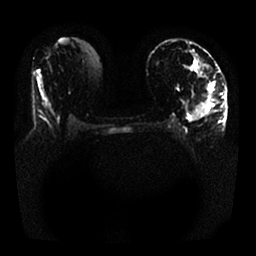
Breast MRI, one axial slice. Position 12 of 25 along the scan axis. Diffusion-weighted series; image 2 of 4 stored at this slice position (different b-values; order by instance number). 1.5 T. 4 mm slice thickness. 256 × 256 image matrix, field of view 340 × 340 mm. Female patient.
Annotated regions visible in this slice (outlined manually by an expert reader):
- tumour on diffusion-weighted imaging: bounding box <195,83,214,119> (left, top, right, bottom; pixels)